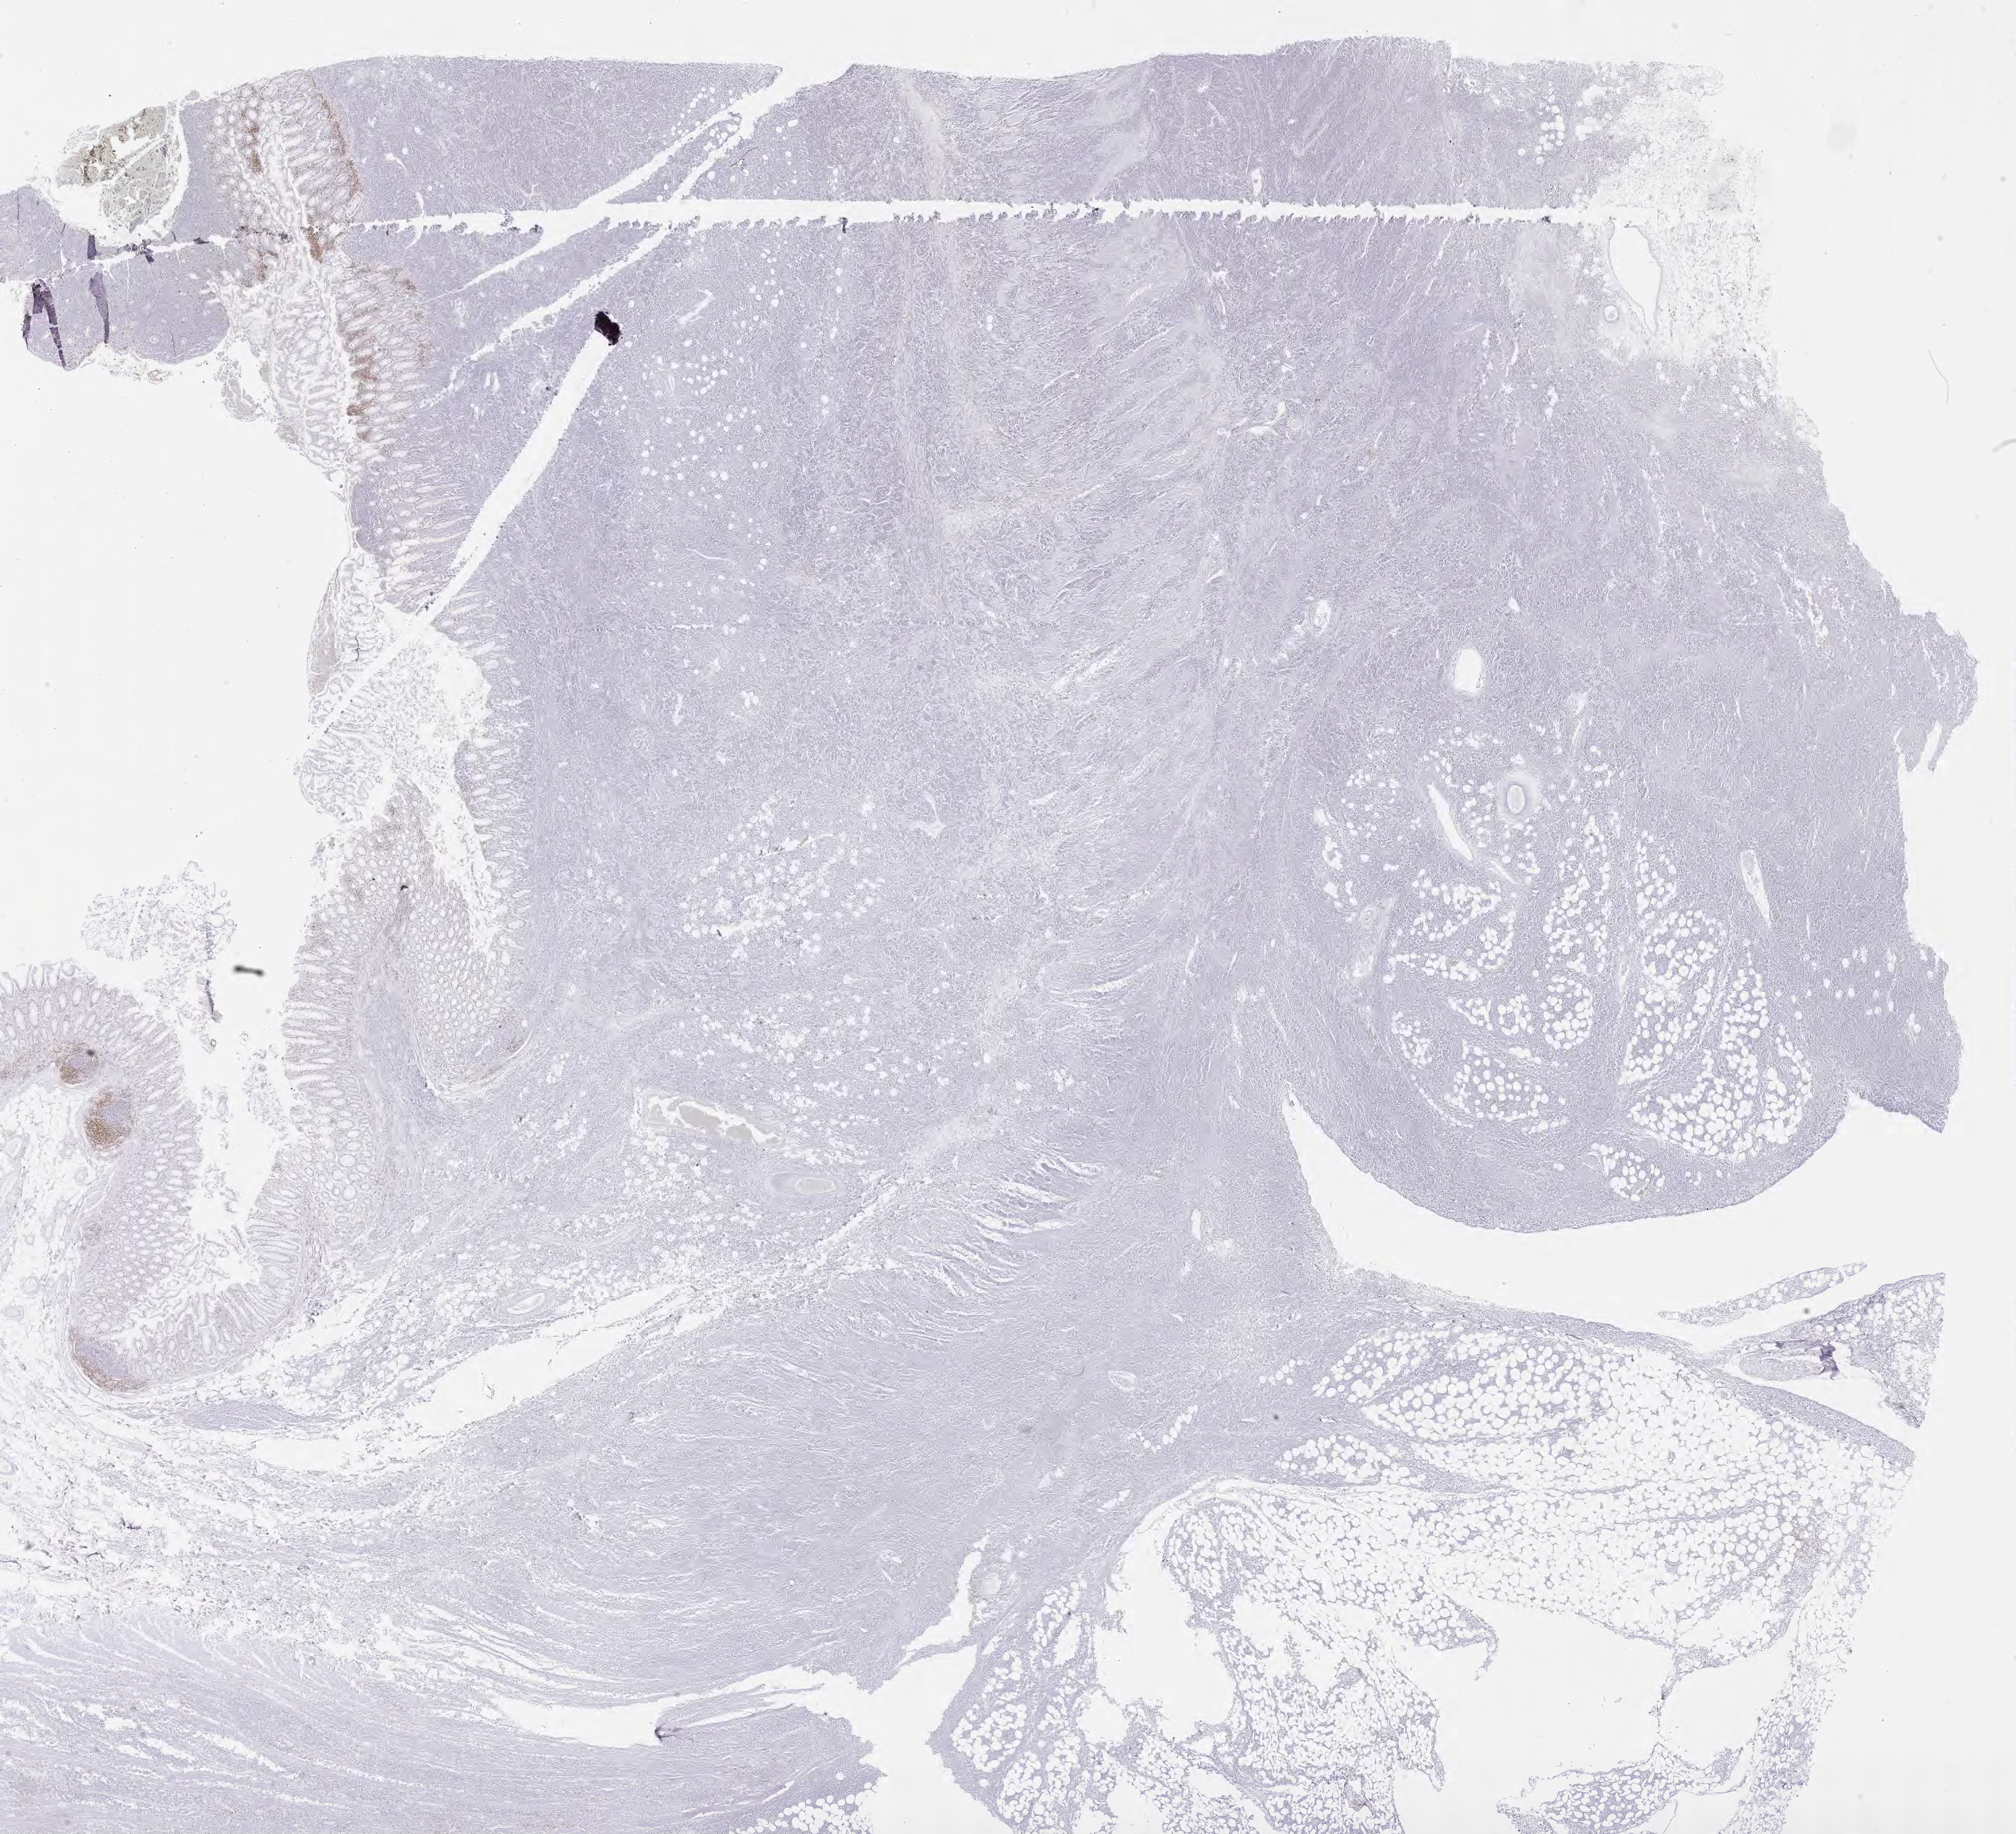
IHC for CD3, whole-slide image — whole scanned area (about 24.2 x 22.0 mm) shown as a low-resolution overview; tumor tissue. Patient male; age 56 years.
Diagnosis: Burkitt lymphoma, NOS.